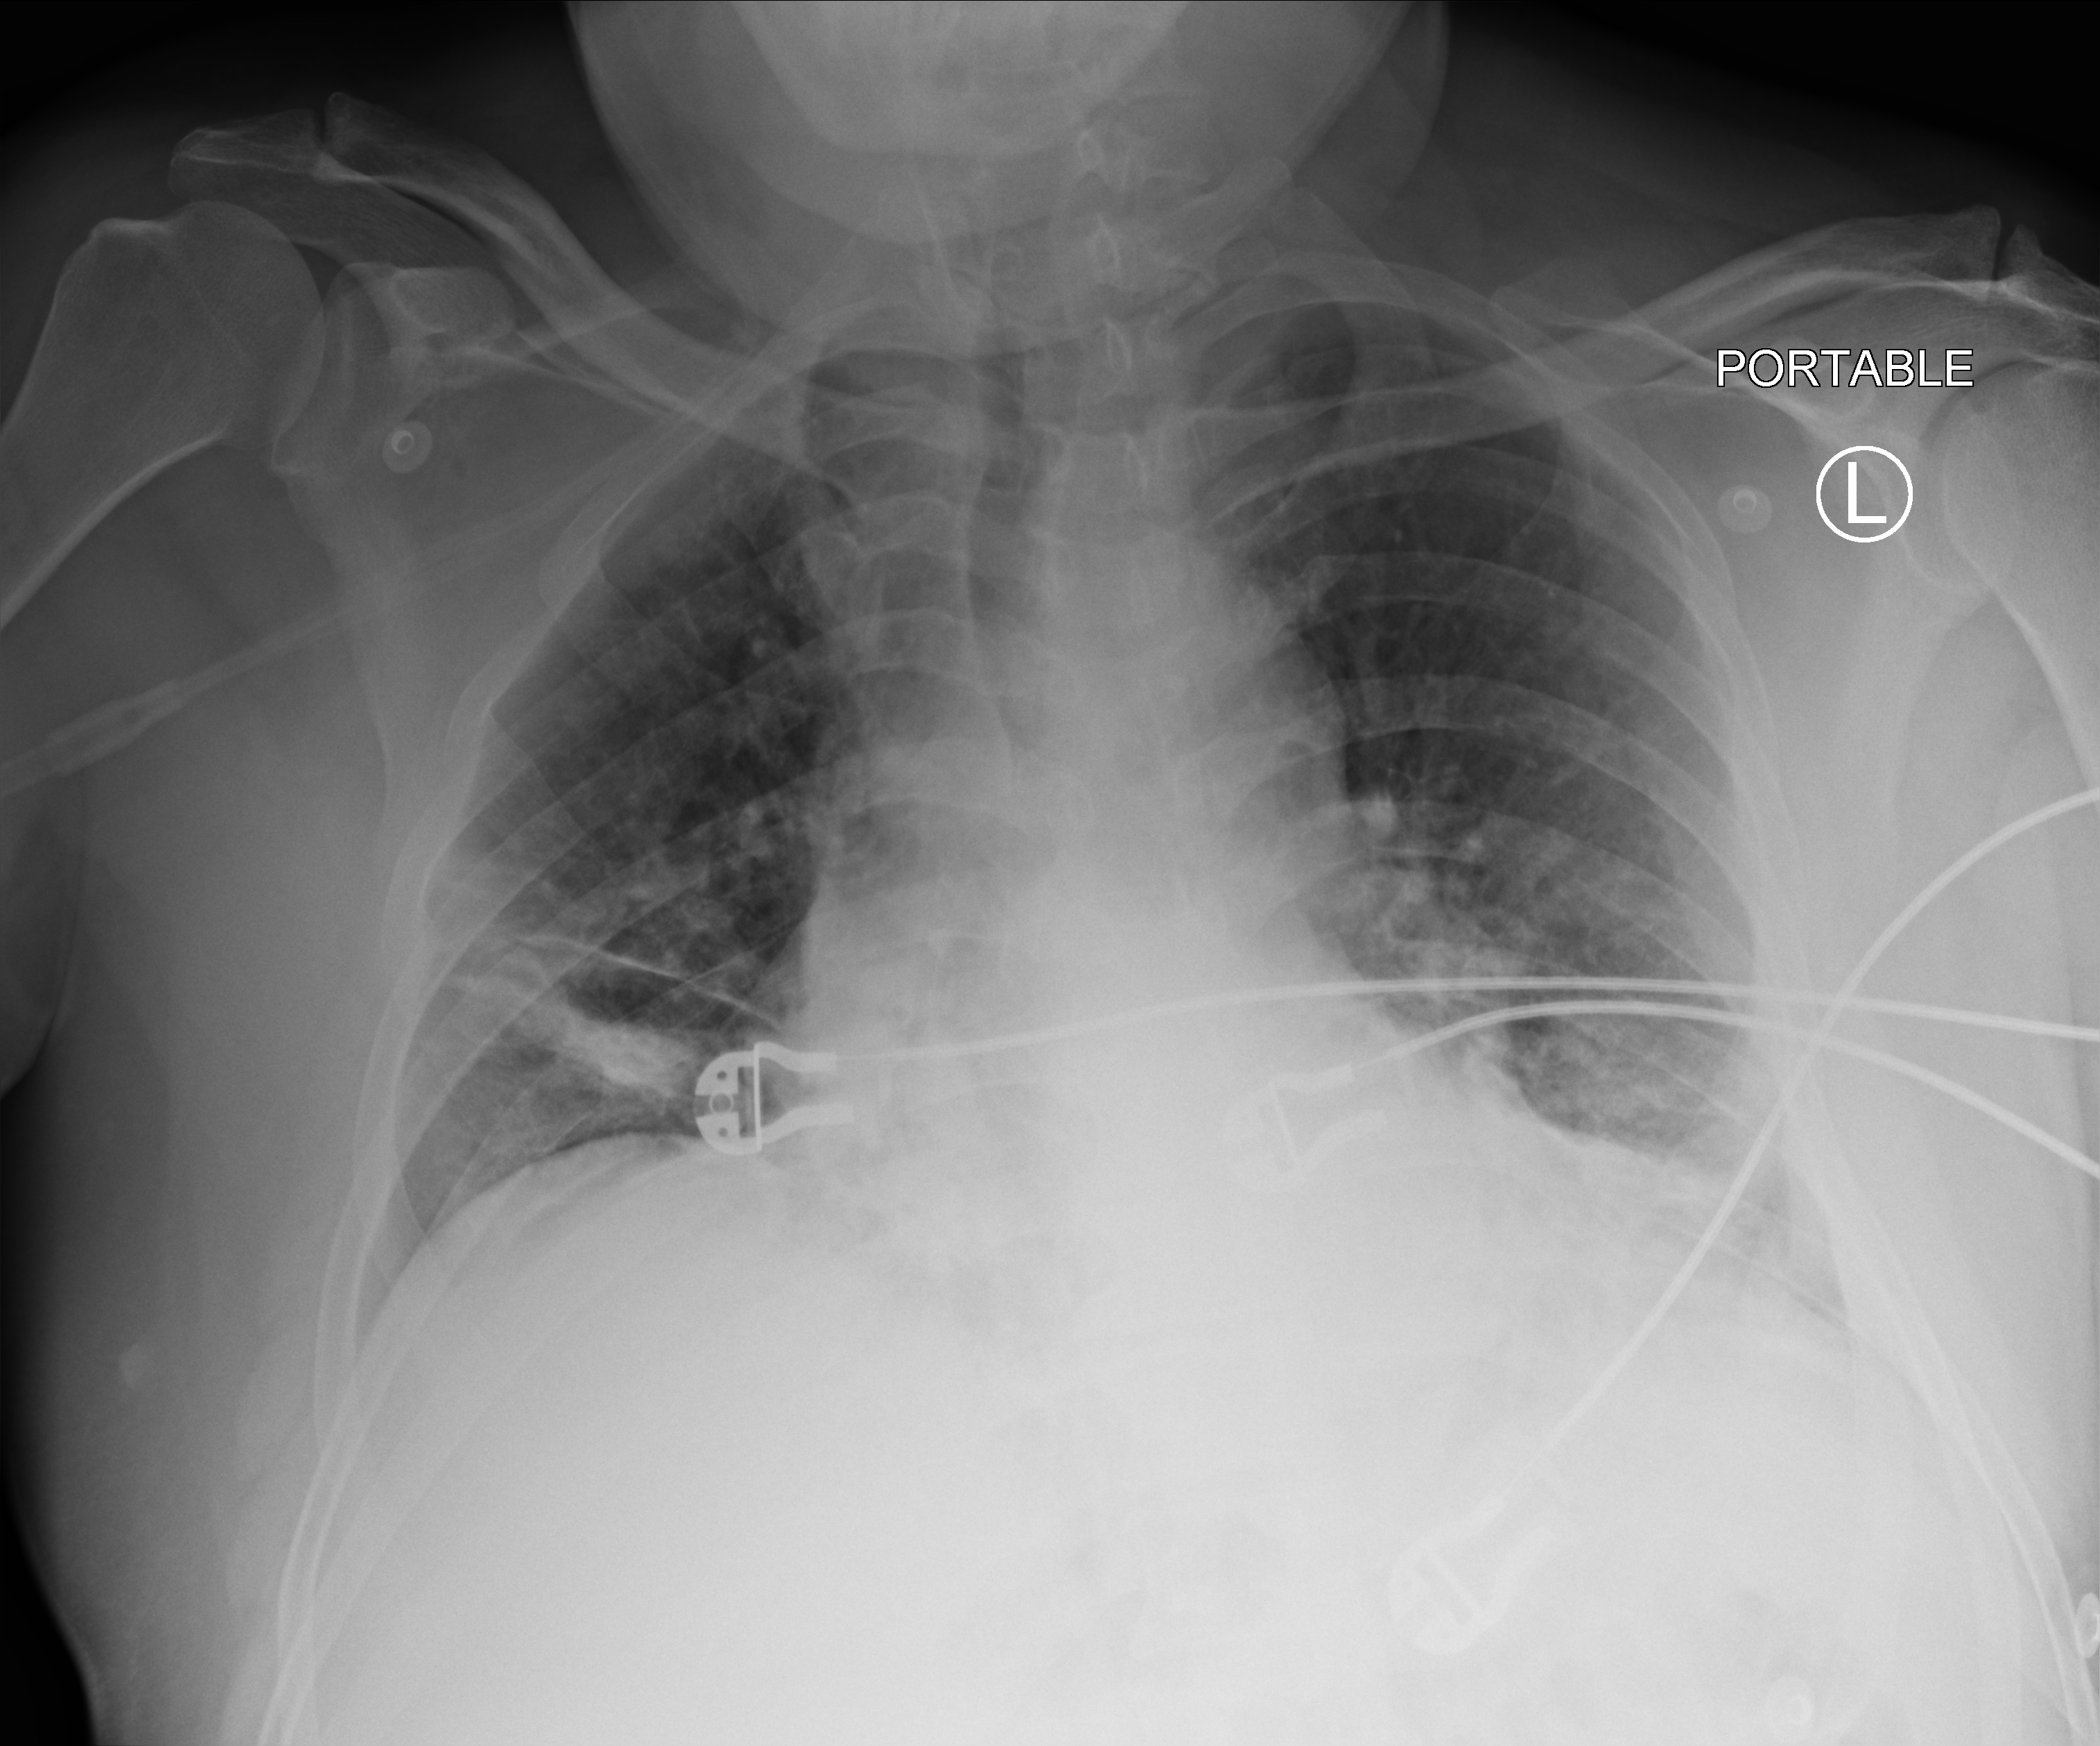
Bedside chest radiograph (computed radiography). Patient hospitalised with COVID-19; male, aged 18–59 years.
From the hospital-stay record, not from the radiograph (when in the stay this image was taken is not recorded): other chronic lung disease (admission record): no.